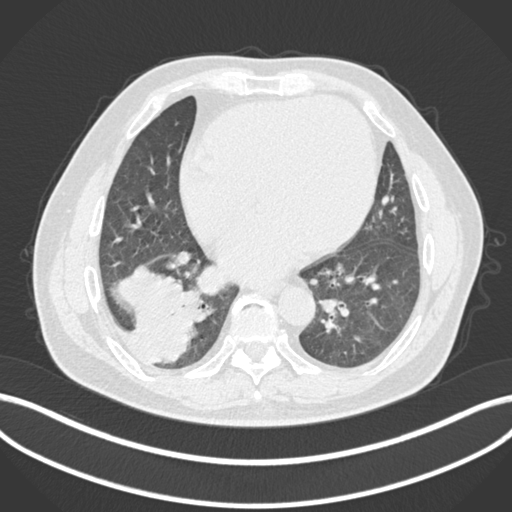
Chest CT, one axial slice; slice 57 of 200 in the series (ordered by position); 120 kVp; lung window (W 1500 / L -600 HU); 1 mm slice thickness; 512 × 512 image matrix, field of view 400 × 400 mm. Male patient, age 59 years.
Annotated regions visible in this slice (rectangle marked by the reading radiologist):
- lung tumour (recorded histology: adenocarcinoma): bounding box <110,257,201,366> (left, top, right, bottom; pixels)